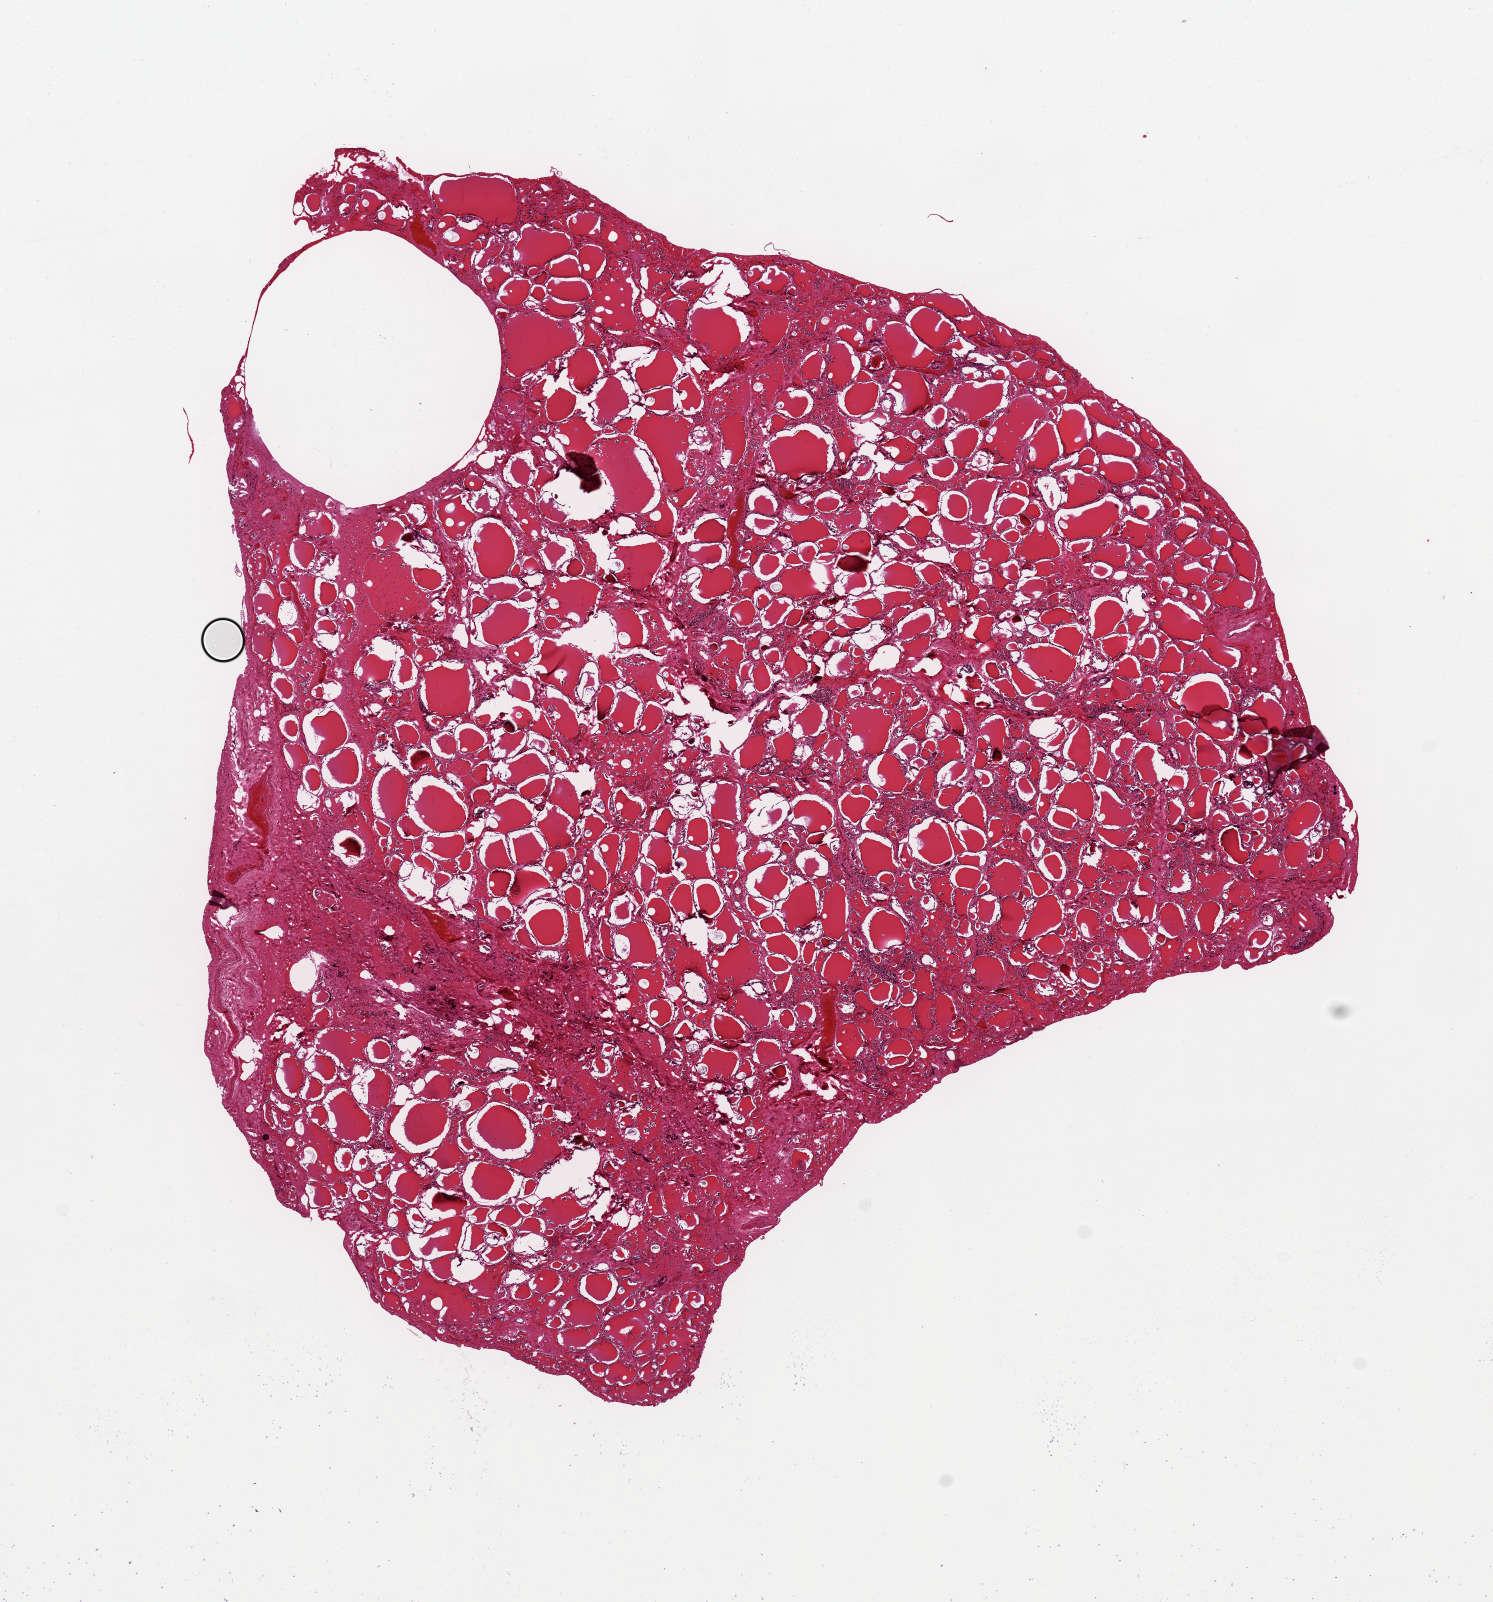
H&E whole-slide image, whole scanned area (about 11.8 x 12.7 mm) shown as a low-resolution overview; PAXgene-fixed, paraffin-embedded tissue; section of thyroid (target tissue); tissue donor sample.
Review note (as recorded): Moderate autolysis.